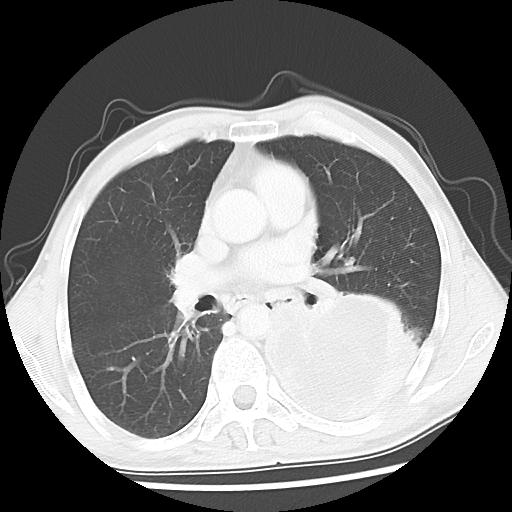
Chest CT, one axial slice. Slice 27 of 52 in the series (ordered by position). Reconstruction kernel LUNG. 120 kVp. Lung window (W 1500 / L -600 HU). 512 × 512 image matrix. Male patient, age 60 years. Case-level facts recorded for this patient, not image findings: clinical TNM (as recorded): T4 N0 M0.
Structures marked on this image (bounding box drawn by a radiologist):
- lung tumour (recorded histology: squamous cell carcinoma): bounding box (x1, y1, x2, y2) in pixels: (238, 274, 425, 445)